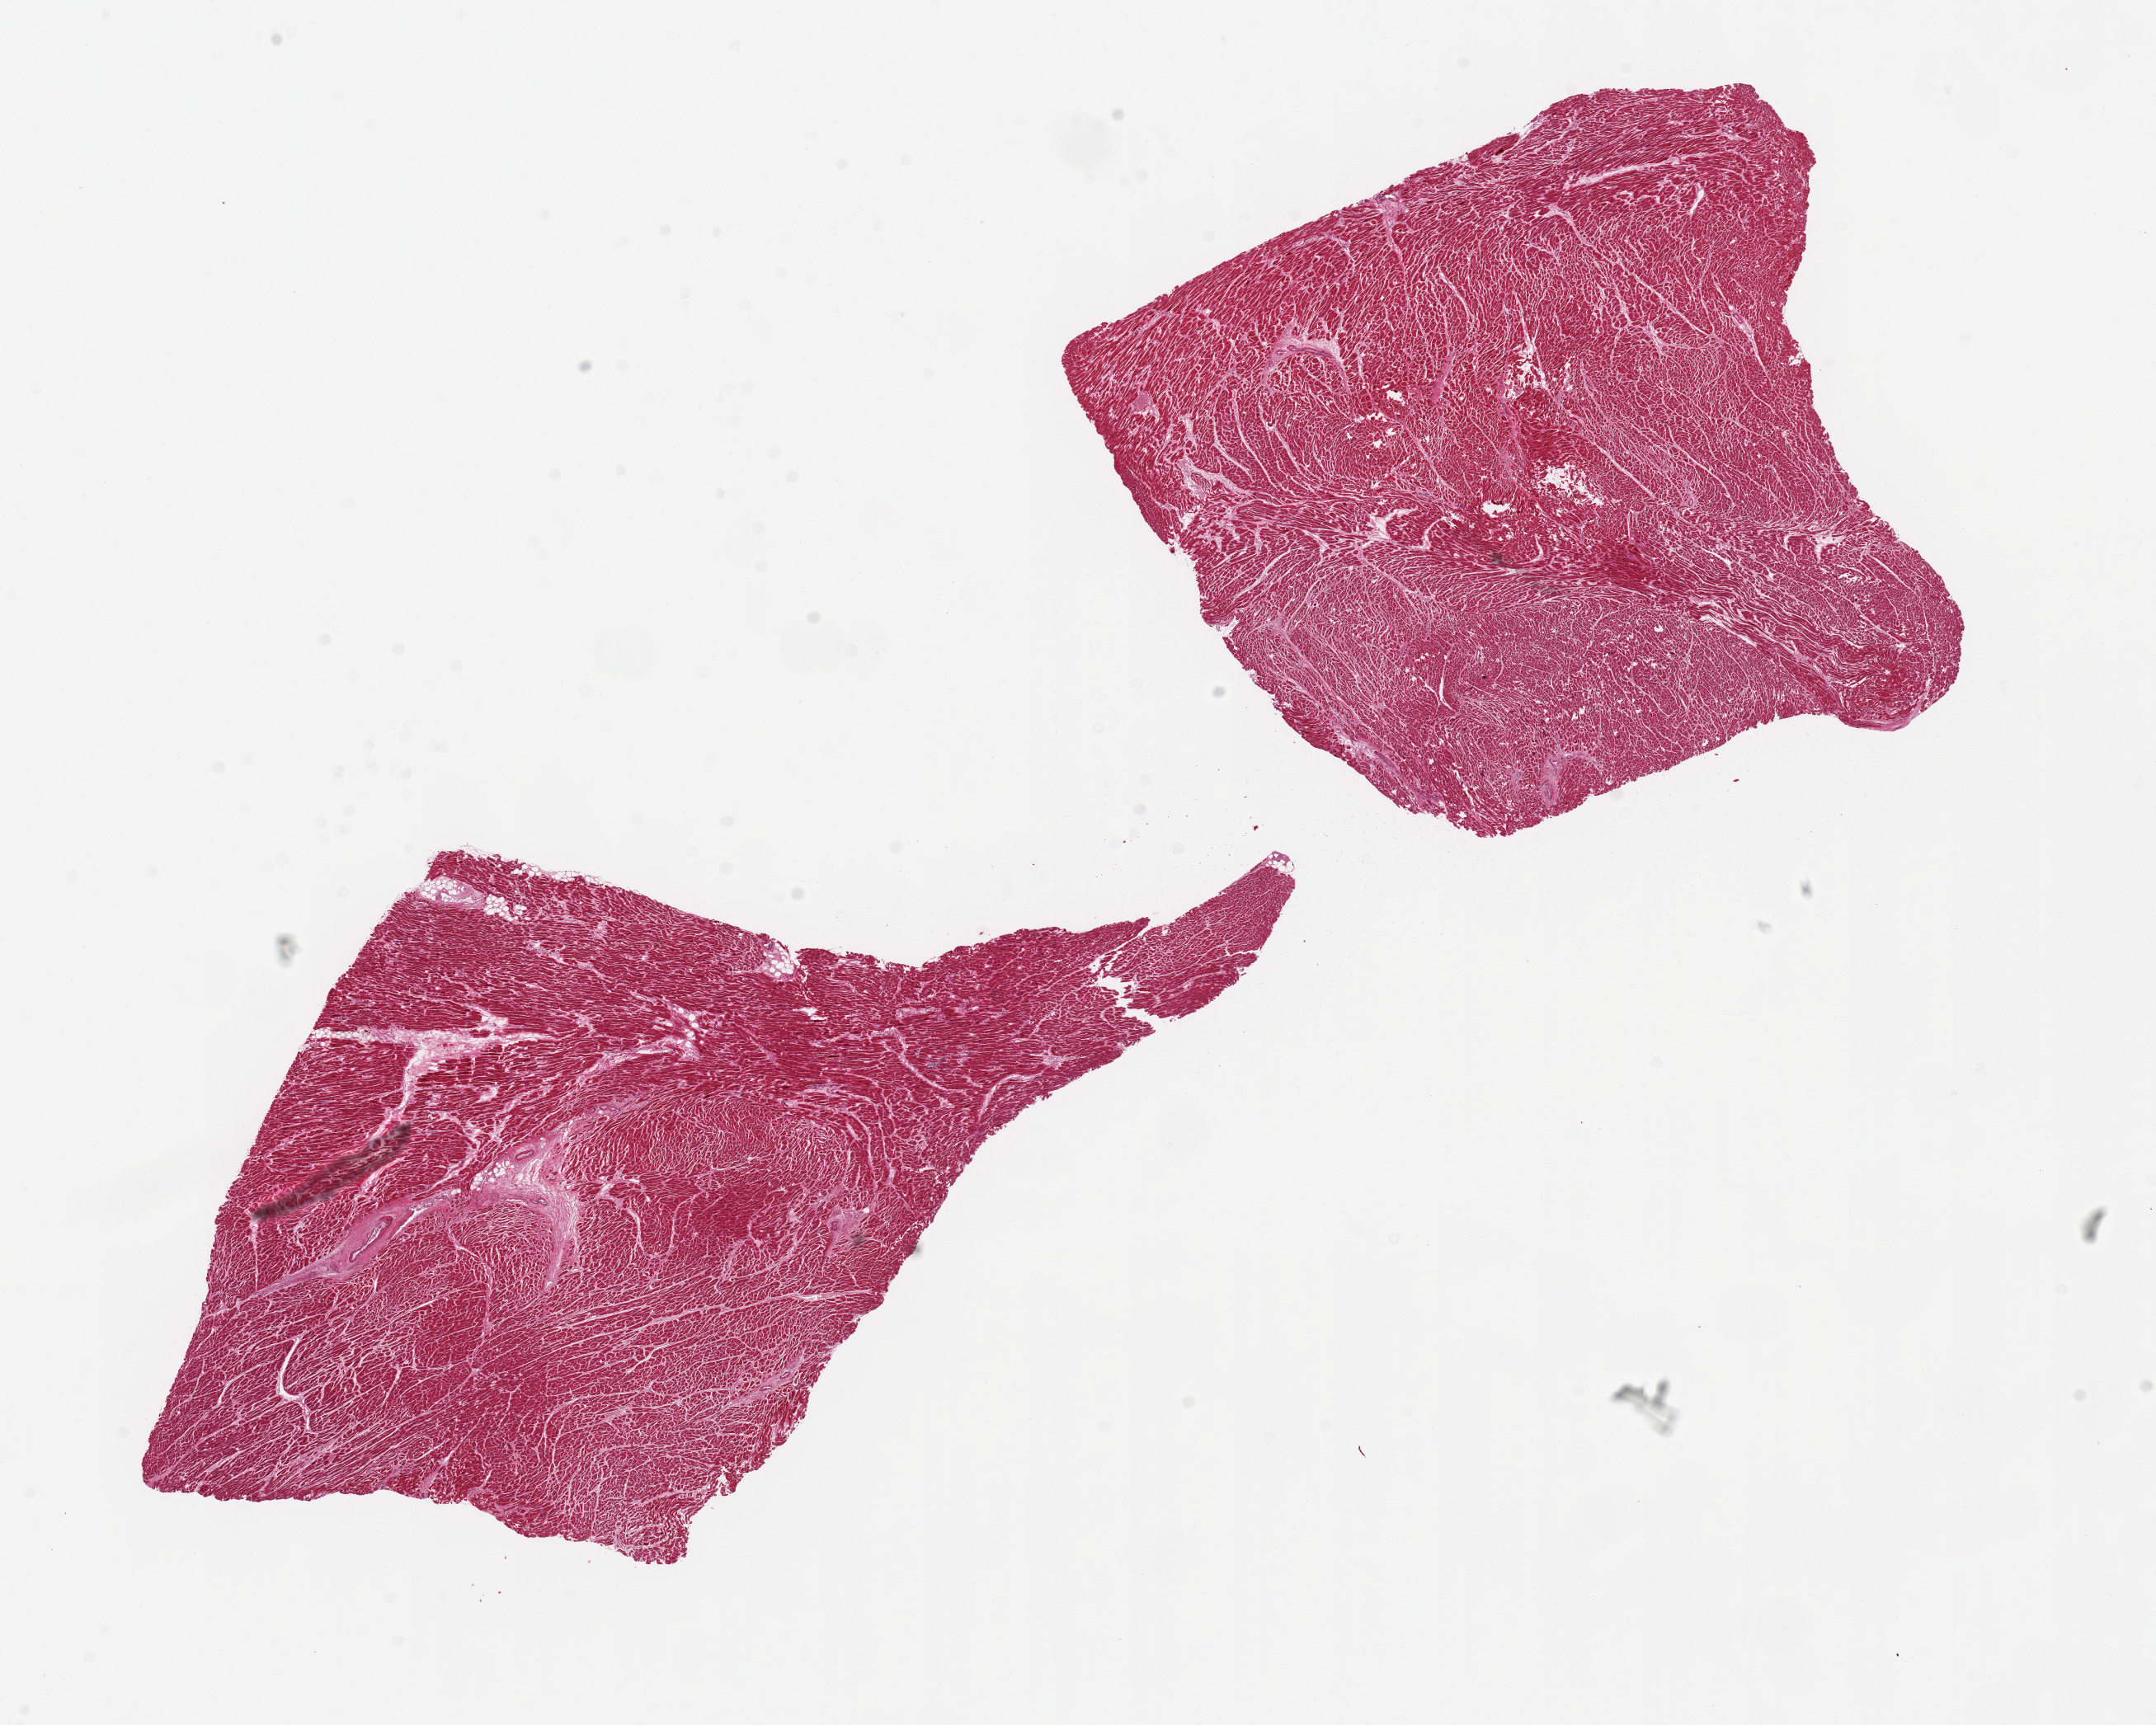
Digitized H&E-stained section, brightfield — shown as a low-resolution overview of the whole scanned area (about 20.7 x 16.5 mm). PAXgene-fixed, paraffin-embedded tissue. Section of heart (target tissue). Donor tissue sample. Female donor.
Reviewer comment on this tissue sample: 2 pieces. 9x9 & 7x7mm; hypertrophied fibers.